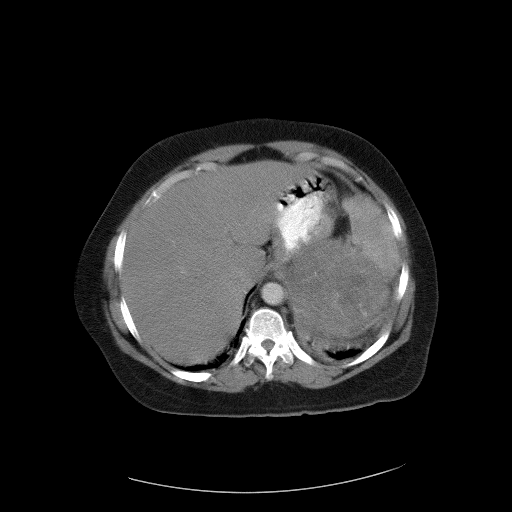
Contrast-enhanced abdominal CT, one axial slice. Position 81 of 90 along the scan axis. Reconstruction kernel FC01. 120 kVp. Intravenous contrast given. Soft-tissue window (W 400 / L 40 HU). 5 mm slice thickness. 512 × 512 image matrix. Female patient, age 55 years. Case-level facts recorded for this patient, not image findings: diagnosis: adrenocortical carcinoma; tumour side: left adrenal; tumour size at pathology: 22 cm; Ki-67 index: 10 %; stage (as recorded): 3.
Structures marked on this image (semi-automatic segmentation, software-assisted and operator-edited):
- mass: bounding box [x1, y1, x2, y2] px = [286, 241, 387, 335]